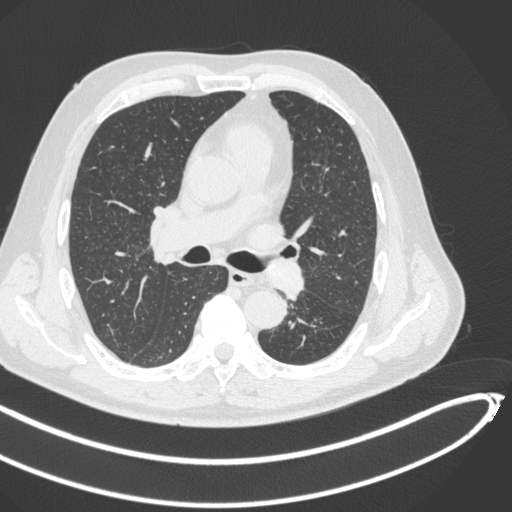
Chest CT, one axial slice. Slice 274 of 466 in the series (ordered by position). Reconstruction kernel B31f. 120 kVp. Lung window (W 1500 / L -600 HU). 1 mm slice thickness. 512 × 512 image matrix, field of view 400 × 400 mm. Male patient, age 64 years. Case-level facts recorded for this patient, not image findings: clinical TNM (as recorded): T1c N0 M0.
Annotated regions visible in this slice (bounding box drawn by a radiologist):
- lung tumour (recorded histology: squamous cell carcinoma): bounding box [x1, y1, x2, y2] px = [266, 257, 308, 300]